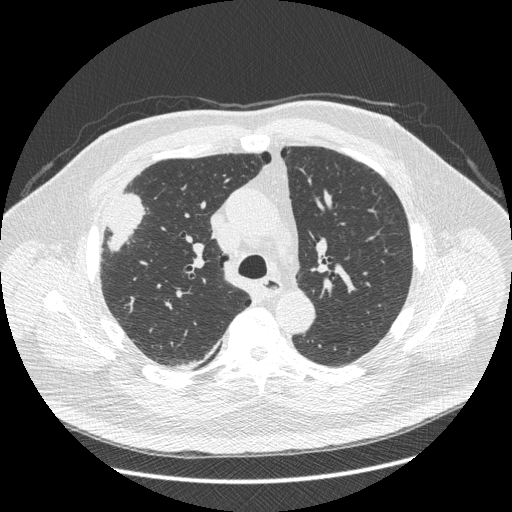
Chest CT (low-dose screening protocol), one axial image; third screening round (two years after baseline); lung window (W 1500 / L -600 HU); 1.25 mm slice thickness; standard (soft-tissue) reconstruction kernel (STANDARD); 512 × 512 image matrix. Male, age 66 years at enrolment.
Lesion marked by an expert reader, box from (x=87, y=191) to (x=146, y=267) px. Screening reader's record for this exam (one nodule recorded; not confirmed to be the boxed lesion): non-calcified nodule or mass ≥4 mm, right upper lobe, 48 × 25 mm, spiculated (stellate) margins, soft tissue attenuation, pre-existing on the prior screen: no. Later outcome: lung cancer diagnosed 35 days after this screen — non-small cell carcinoma, right upper lobe, stage IV (AJCC 6th edition), 50 mm at pathology.